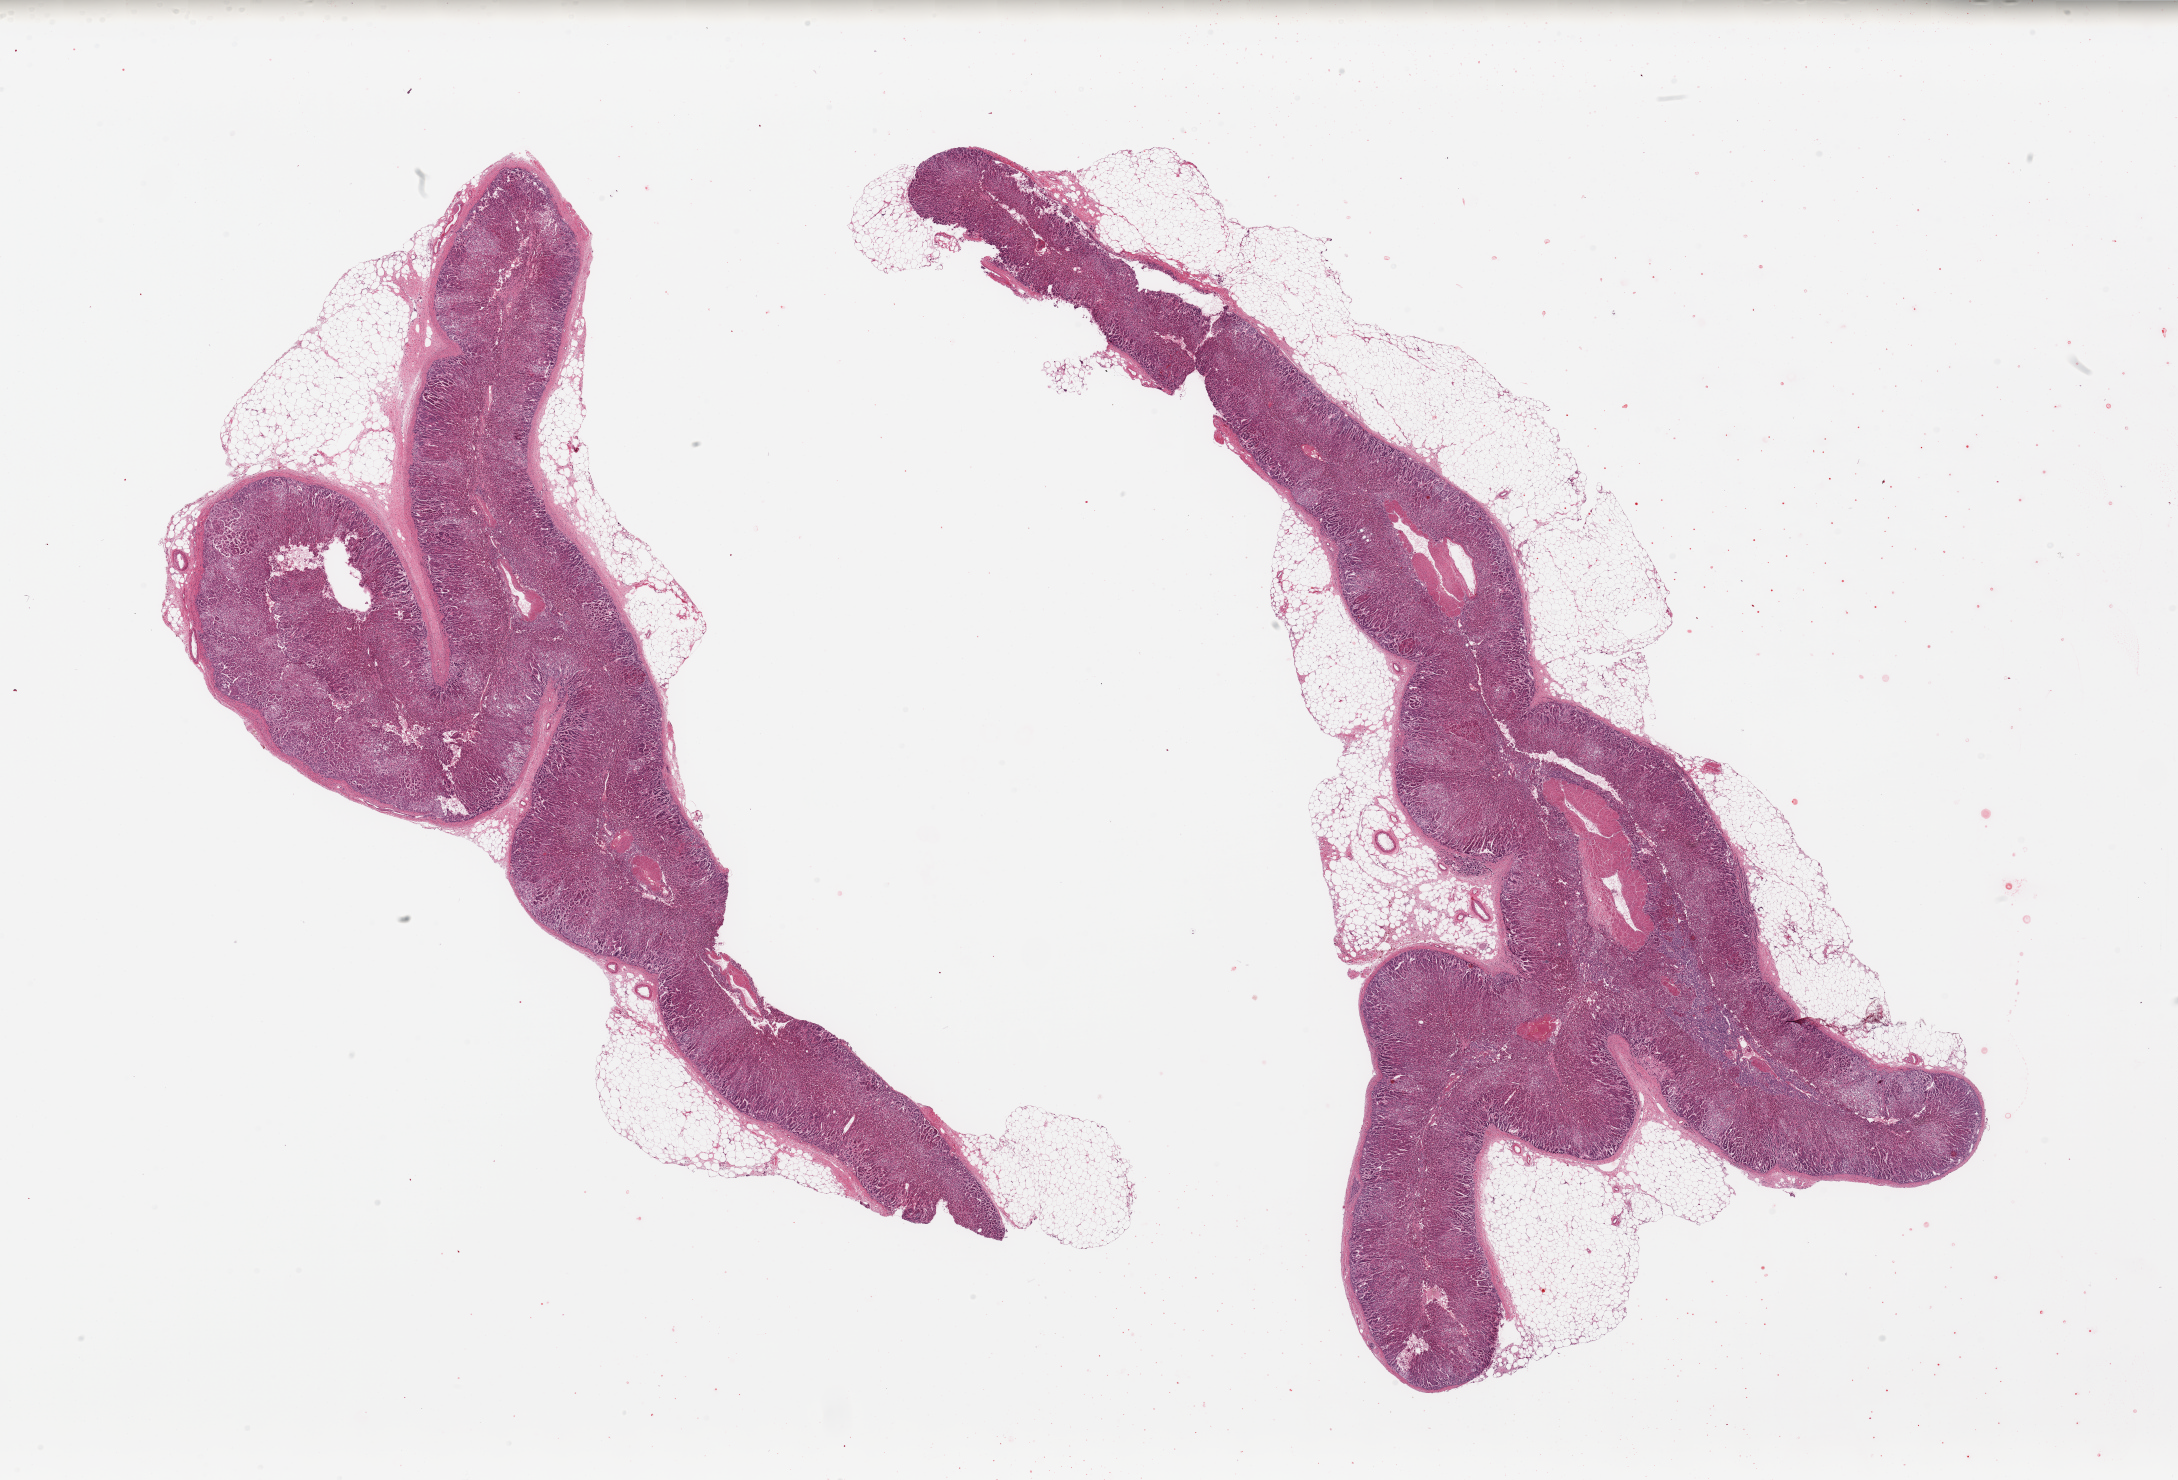
H&E whole-slide image, a low-resolution overview of the entire scanned area, about 34.5 x 23.4 mm (acquisition: 20x scan), PAXgene-fixed paraffin-embedded (PFPE) section, sampled site (target tissue): adrenal gland, tissue donor sample. Donor: male.
• reviewer comment on this tissue sample: 2 pieces, mainly cortex; well fixed; Focal medulla; Rim of adherent fat up to ~2mm